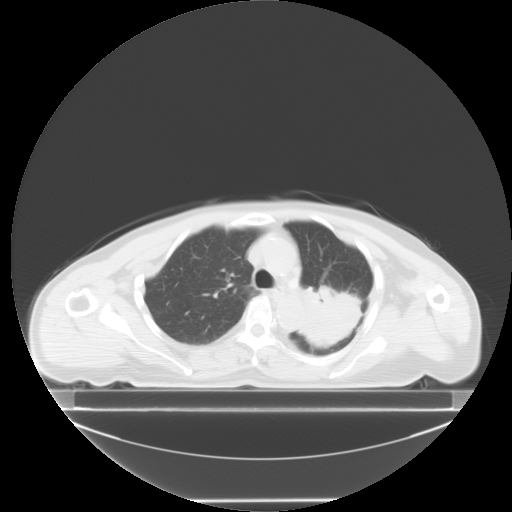
Chest CT, one axial slice; position 8 of 24 along the scan axis; reconstruction kernel STANDARD; 120 kVp; lung window (W 1500 / L -600 HU); 5 mm slice thickness; 512 × 512 image matrix. Patient: female, 74 years. Case-level facts recorded for this patient, not image findings: clinical TNM (as recorded): T3 N1 M1c.
Outlined on this slice (bounding box drawn by a radiologist):
- lung tumour (recorded histology: small cell carcinoma): bounding box <297,282,366,349> (left, top, right, bottom; pixels)